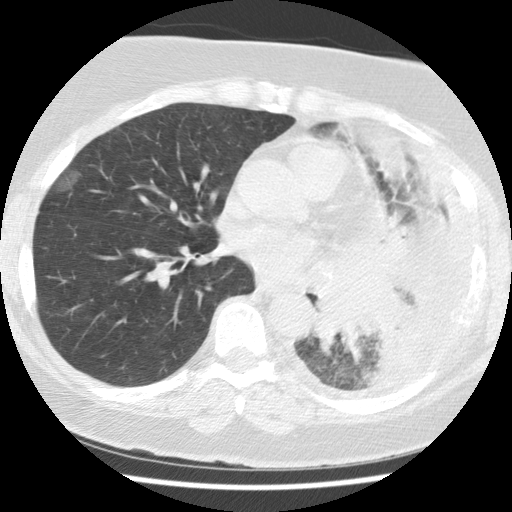
Chest CT (low-dose screening protocol), one axial image. Baseline annual screen. Lung window (W 1500 / L -600 HU). 2.5 mm slice thickness. Standard (soft-tissue) reconstruction kernel (STANDARD). Female participant, aged 65 years at enrolment. Current smoker at enrolment.
- Expert reader's lesion annotation, bounding box (x1, y1, x2, y2) in pixels: (304, 282, 412, 370).
- Screening reader's record for this exam (one nodule recorded; not confirmed to be the boxed lesion): non-calcified nodule or mass ≥4 mm, left lower lobe, 74 × 48 mm, spiculated (stellate) margins, soft tissue attenuation.
- Official screen result: positive, change unspecified: nodule(s) >= 4 mm or enlarging nodule(s), mass(es), or other non-specific abnormalities suspicious for lung cancer.
- Later outcome: lung cancer diagnosed 13 days after this screen — adenocarcinoma, NOS, left lower lobe, stage IV (AJCC 6th edition), 74 mm at pathology.